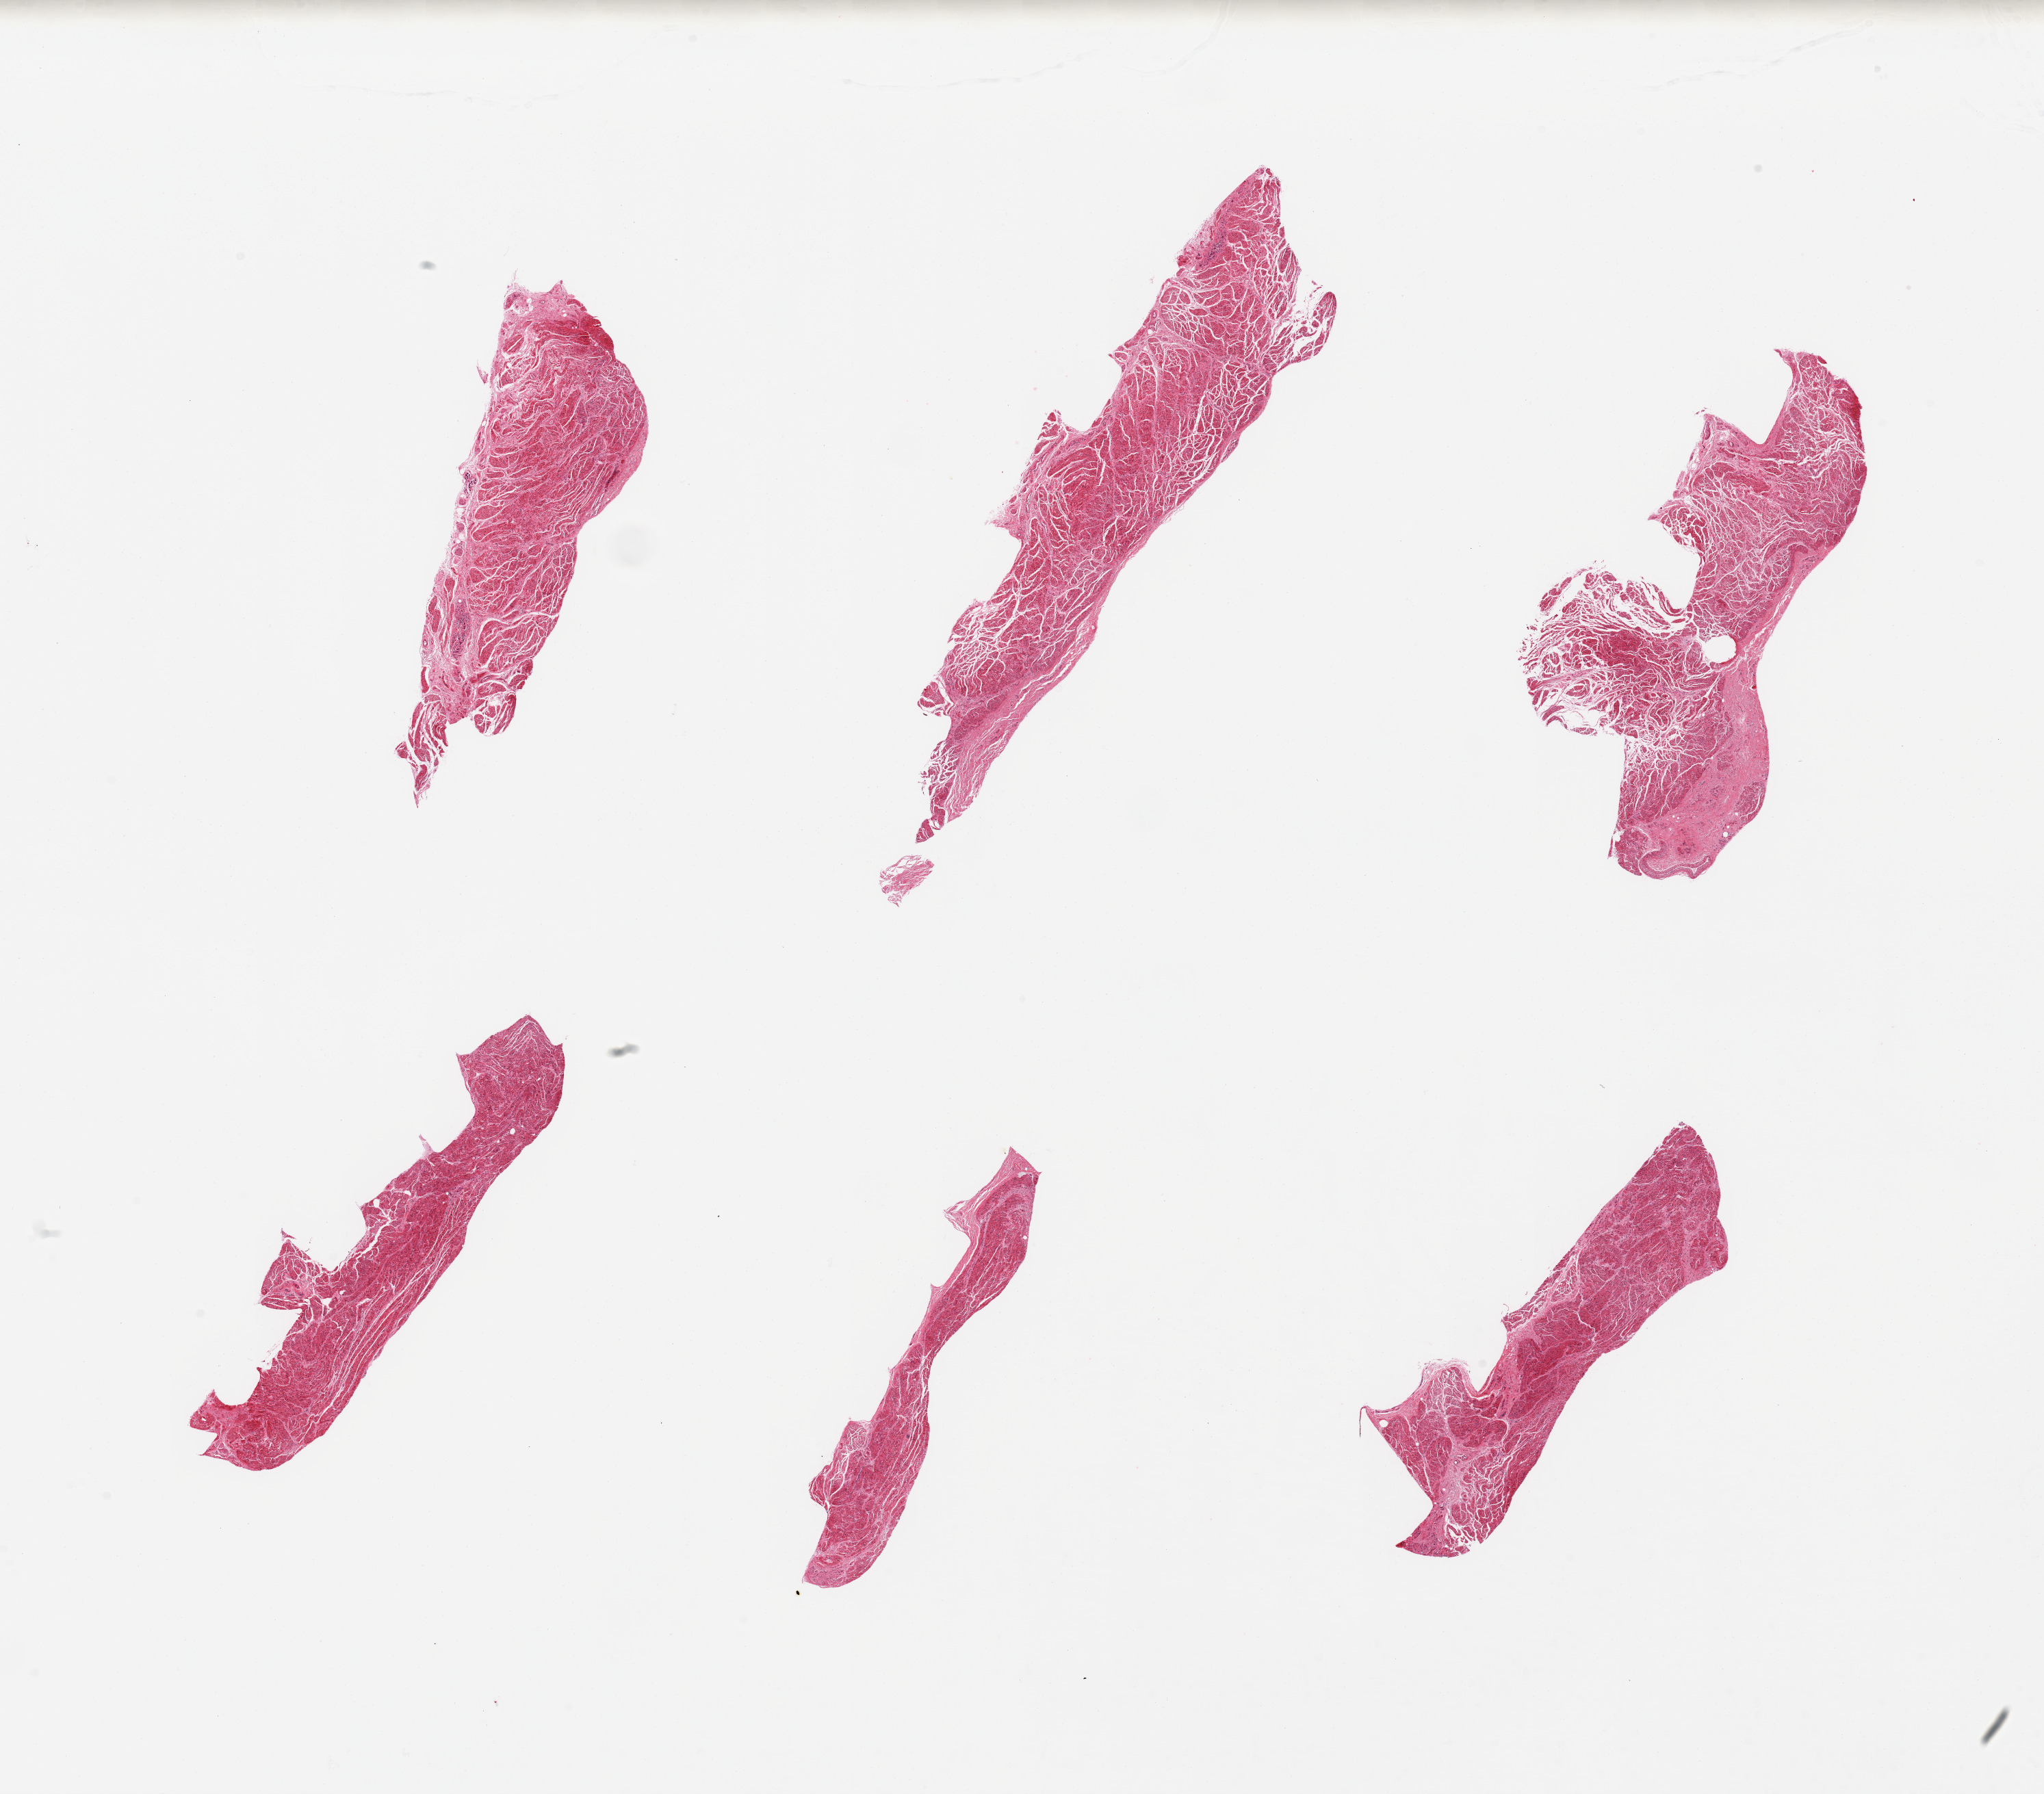
Hematoxylin and eosin (H&E) whole-slide image — shown as a low-resolution overview of the whole scanned area (about 23.6 x 20.7 mm, acquisition: 20x scan); PAXgene-fixed, paraffin-embedded tissue; sampled site (target tissue): gastroesophageal junction; tissue donor sample. Donor: male.
Pathologist's review note for this sample: 6 pieces; largely muscle with a focus of fibrous submucosa in 1 piece.